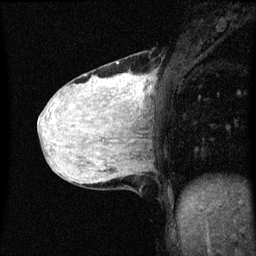
Breast MRI (dynamic contrast-enhanced), one sagittal slice. Slice 22 of 60 in the series (ordered by position). Dynamic contrast-enhanced series, image 2 of 3 at this slice position (ordered by acquisition). 1.5 T. TE 4.2 ms, TR 8.4 ms. 256 × 256 image matrix, field of view 200 × 200 mm. Patient: female, 36 years.
Structures marked on this image (semi-automatically segmented with operator editing):
- analysis volume of interest (the breast-tissue region the enhancement analysis was run in; not a lesion): bounding box [x1, y1, x2, y2] px = [48, 62, 155, 151]
- tumour enhancement mask (voxels above the 70 % enhancement threshold inside the analysis volume of interest): [134, 80, 145, 99]